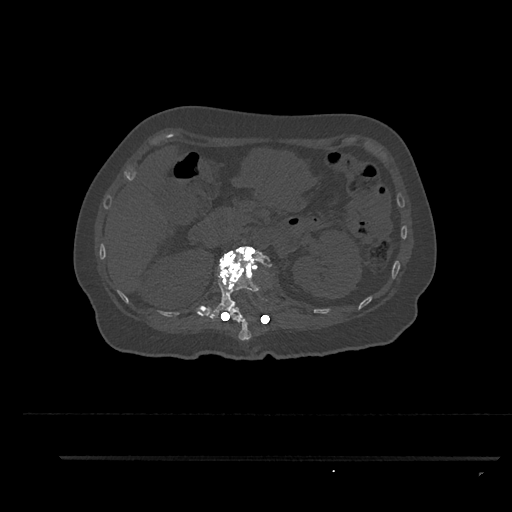
CT including the spine, one axial slice; slice 230 of 797 in the series (ordered by position); reconstruction kernel Br40s/3; 120 kVp; bone window (W 1800 / L 400 HU); 512 × 512 image matrix. Female patient, age 44 years. From the clinical record (not read from this slice): primary cancer: renal.
Structures marked on this image (semi-automatic segmentation, software-assisted and operator-edited):
- L1 vertebra: bounding box [x1, y1, x2, y2] px = [208, 246, 272, 322]
- T12 vertebra: [221, 308, 253, 341]